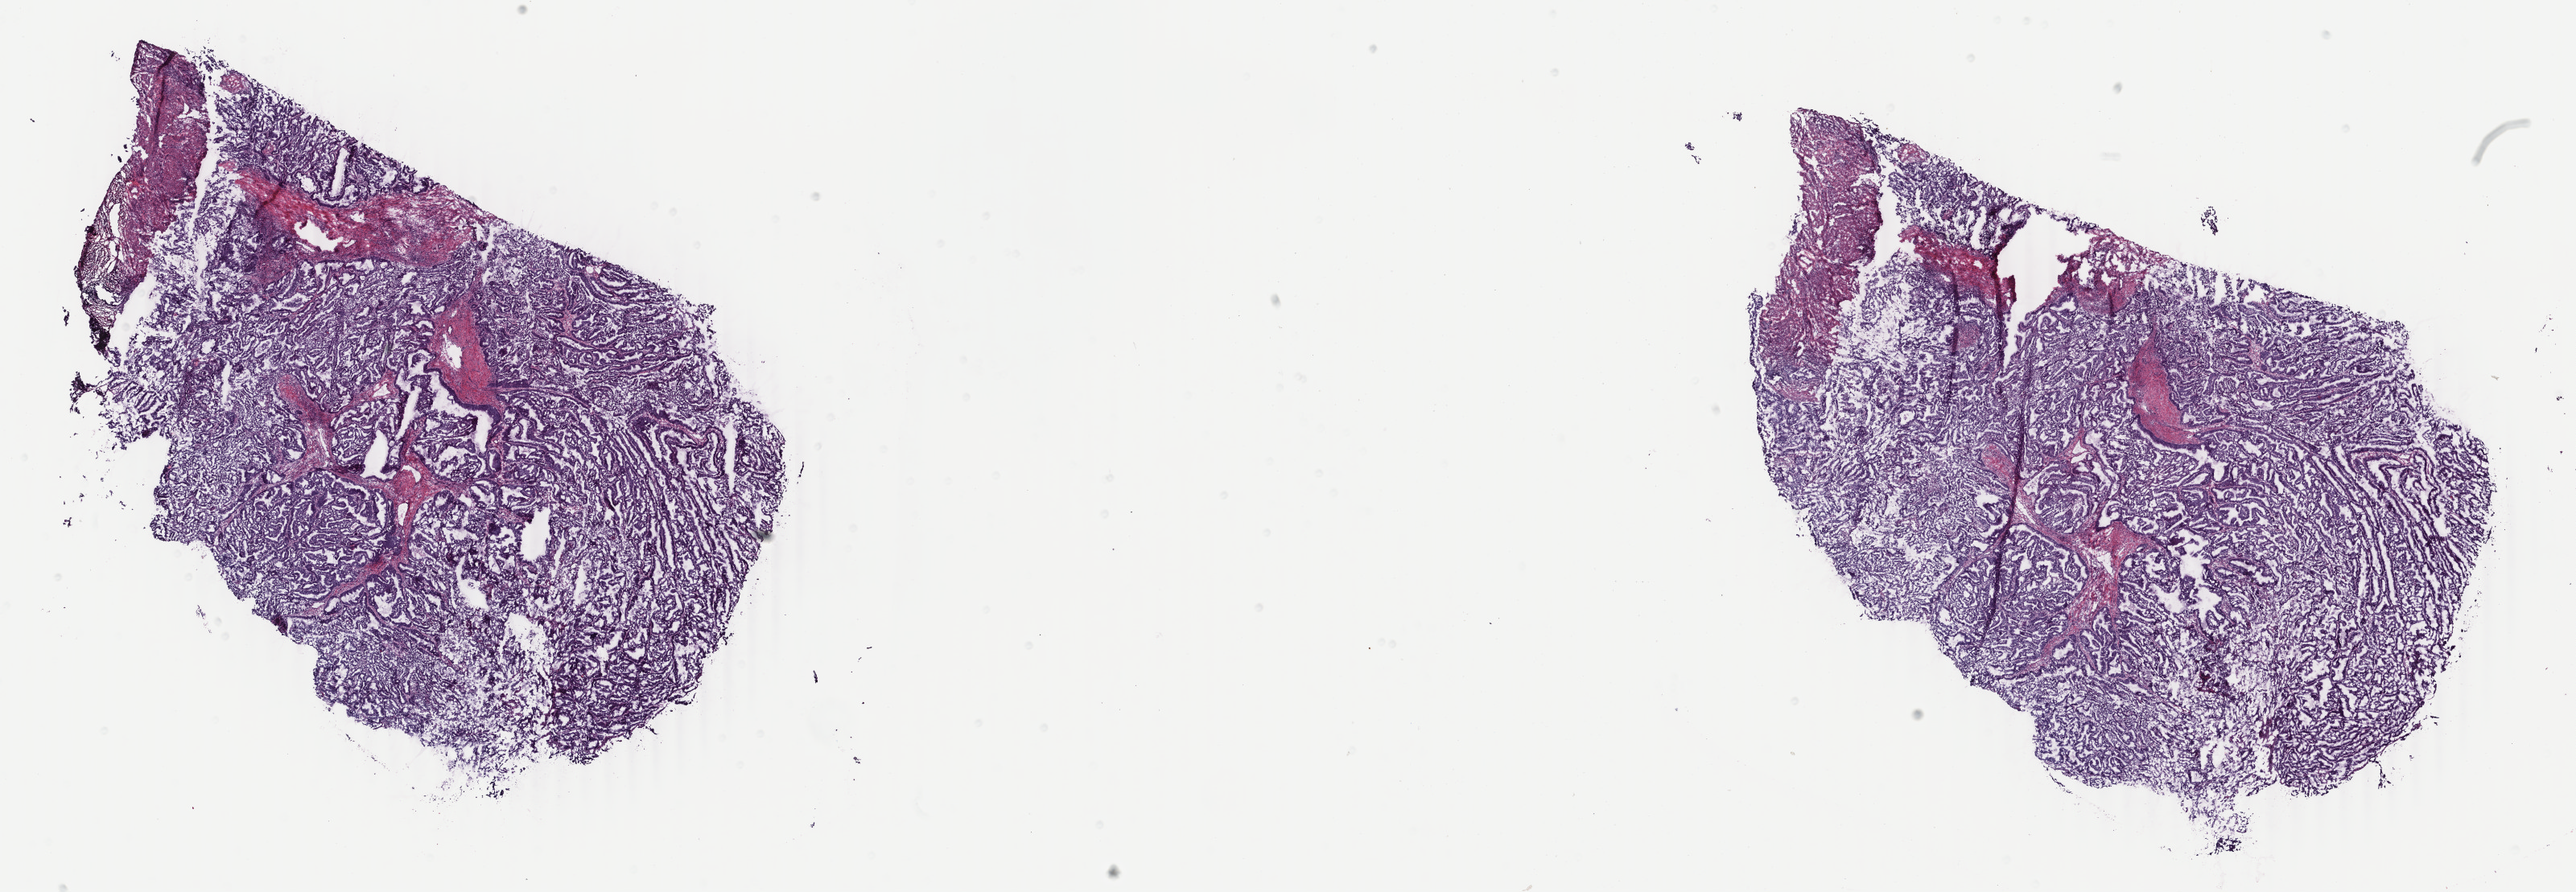
Hematoxylin and eosin (H&E) stained whole-slide image — whole scanned area (about 25.5 x 8.8 mm, from a 40x scan) shown as a low-resolution overview. Frozen section. Sample: primary tumour, uterus. Patient: female, age at initial diagnosis 53 years. Histologic grade: G2 (moderately differentiated). Slide review estimates, as recorded: tumour cells 90%, tumour nuclei 85%, normal cells 10%, stromal cells 0%, necrosis 0%. Infiltration values recorded for this section: lymphocyte infiltration 0%, monocyte infiltration 0%, neutrophil infiltration 0%.
• pathologic diagnosis: Endometrioid adenocarcinoma, NOS
• FIGO stage: IA